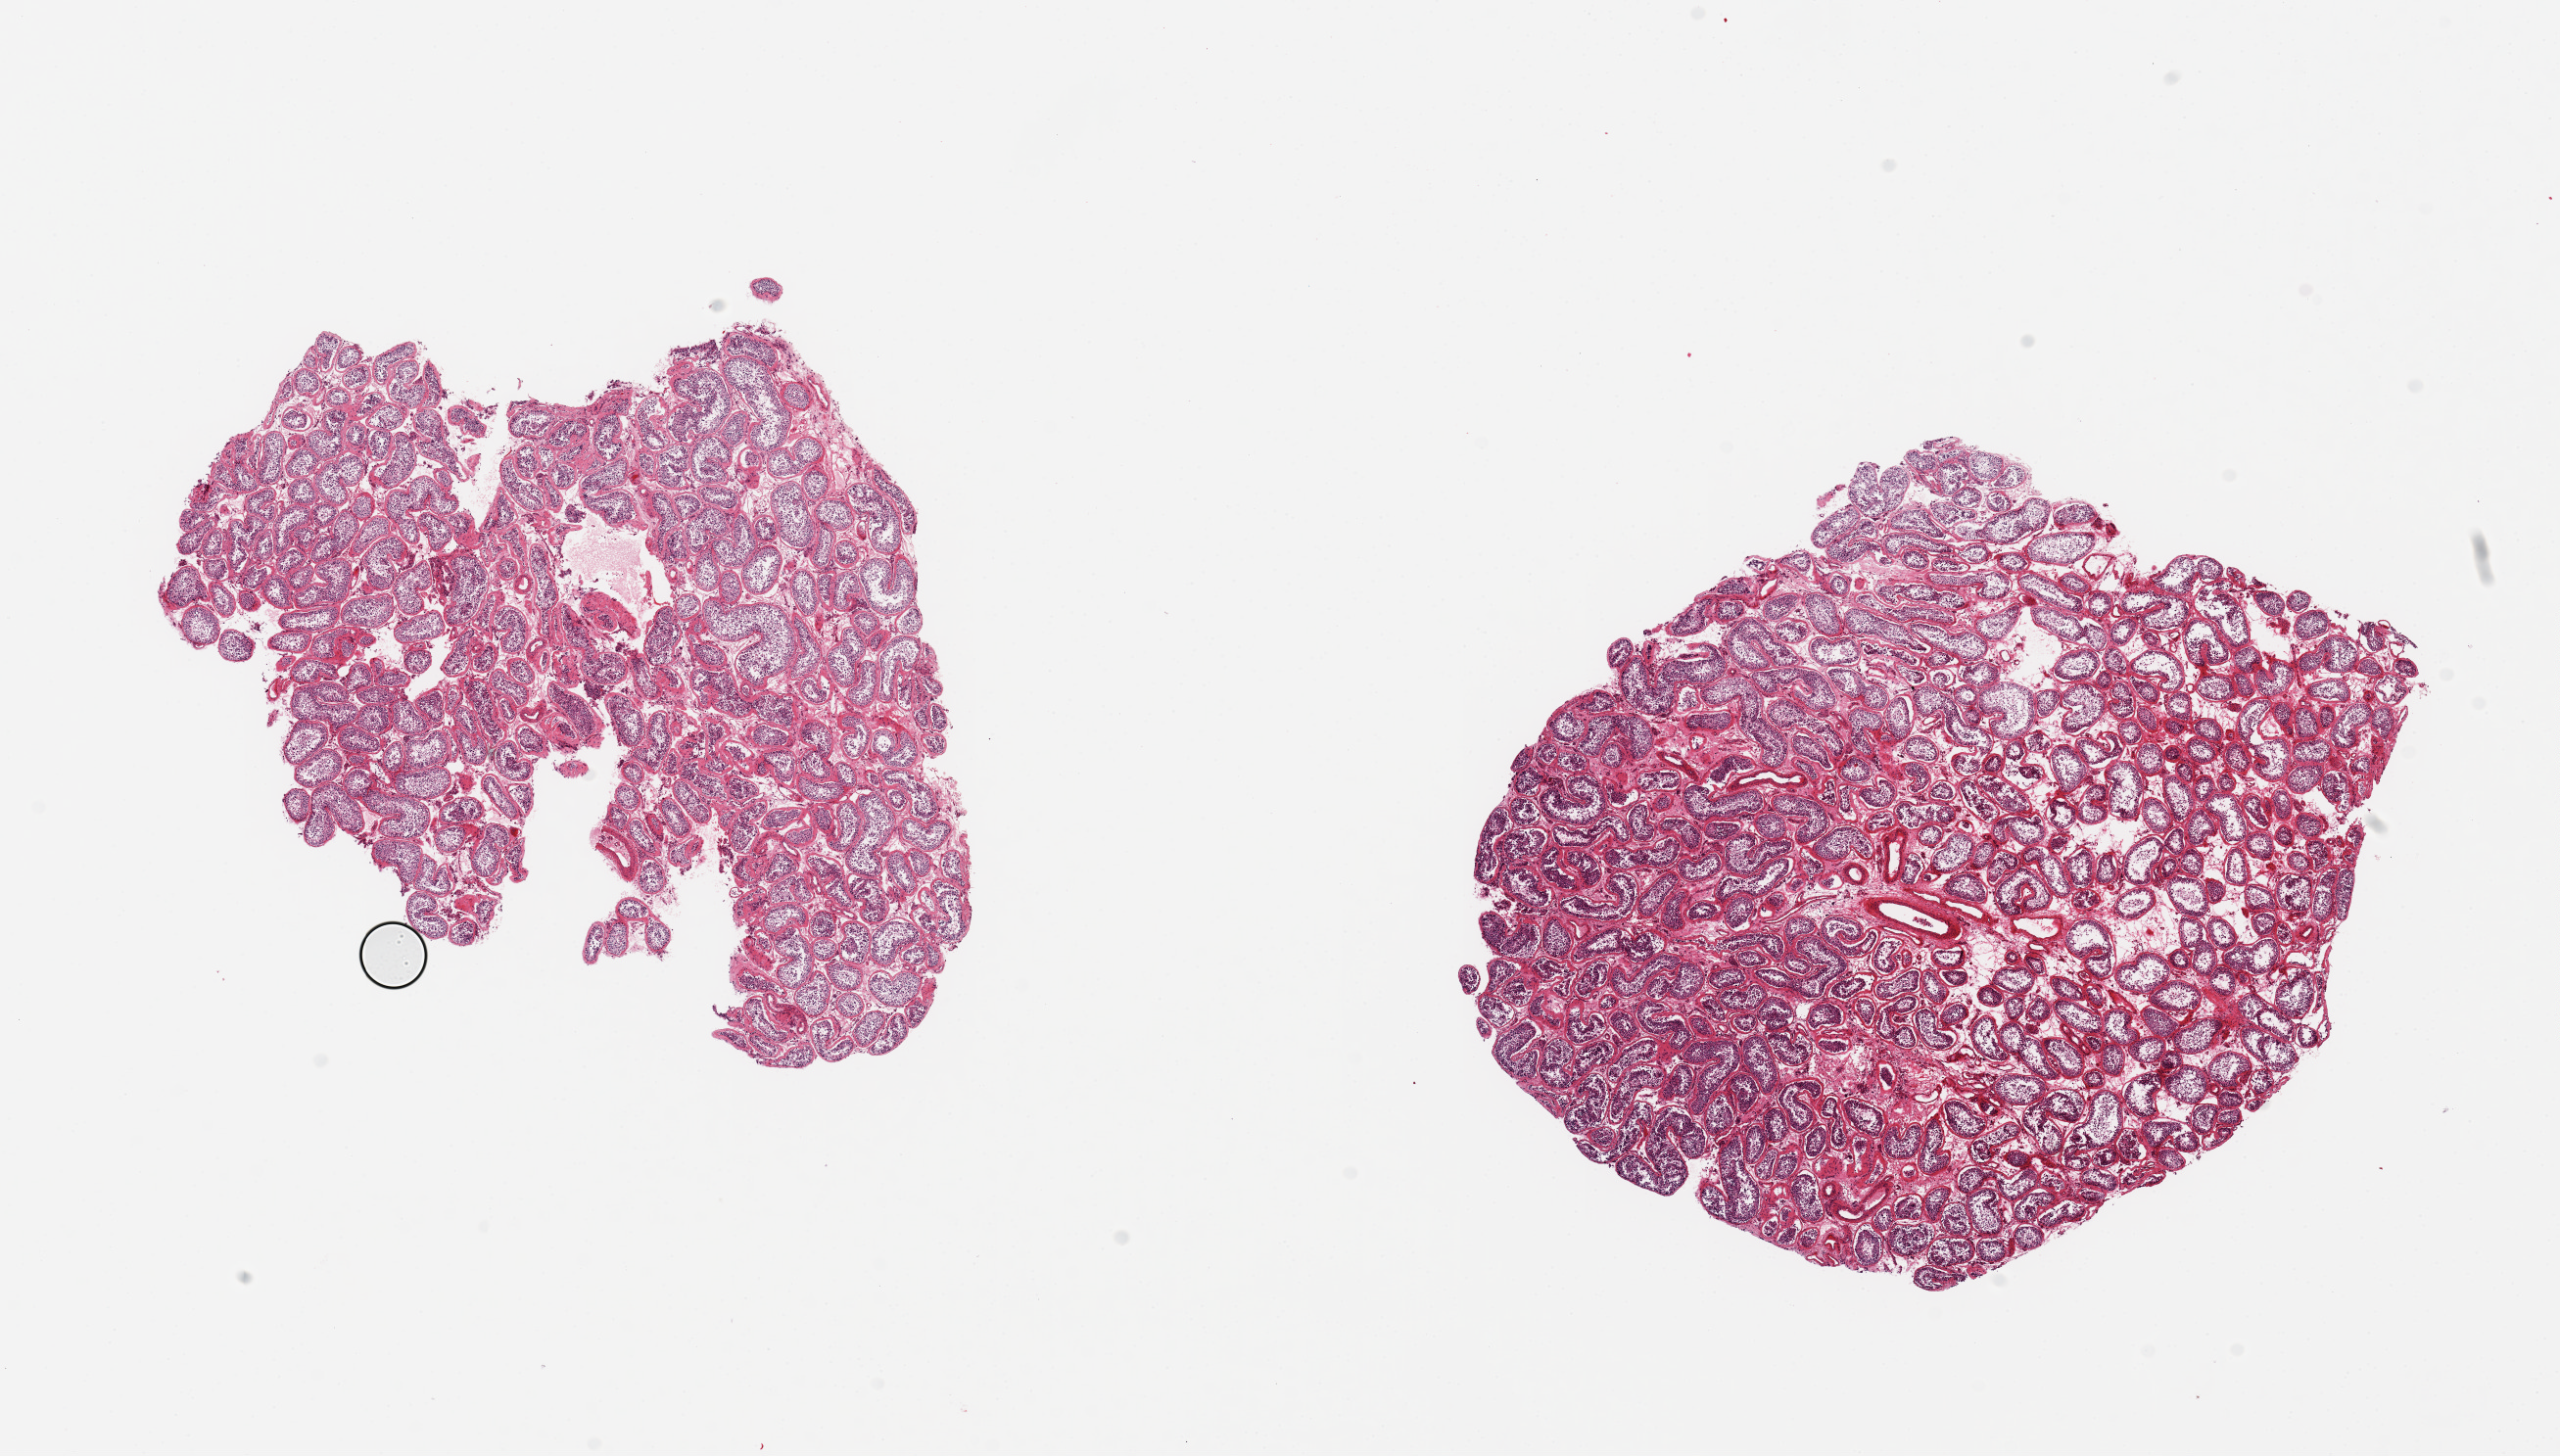
Digitized hematoxylin and eosin (H&E)-stained section, brightfield, whole scanned area (about 20.7 x 11.8 mm, acquisition: 20x scan) shown as a low-resolution overview. PAXgene-fixed paraffin-embedded (PFPE) section. Section of testis (target tissue). Donor tissue sample. Donor: male.
Reviewer comment on this tissue sample: 2 pieces ~7x6mm. Spermatogenesis present, poorly preserved.